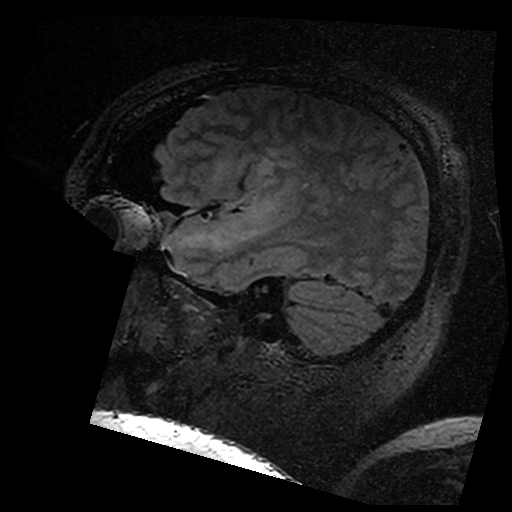
Brain MRI from a brain-tumour surgery series, one sagittal slice. Position 128 of 176 along the scan axis. T2 FLAIR. 512 × 512 image matrix. From the clinical record (not read from this slice): histopathology: Astrocytoma; WHO grade: 3; IDH mutation: yes; tumour location: Left Insular.
Outlined on this slice (expert manual segmentation):
- residual tumour: bounding box [x1, y1, x2, y2] px = [223, 156, 294, 183]